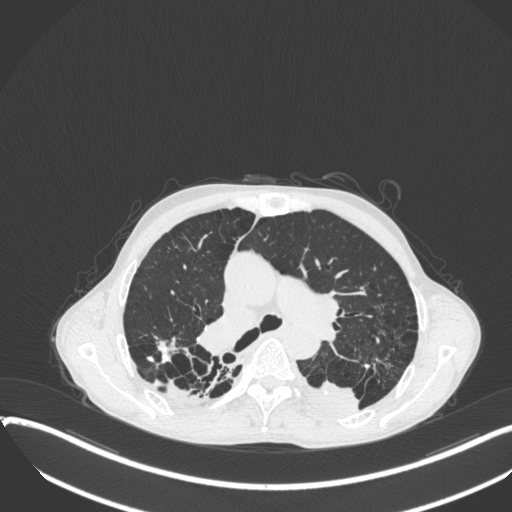
Chest CT, one axial slice. Slice 250 of 400 in the series (ordered by position). Reconstruction kernel B31f. Lung window (W 1500 / L -600 HU). 512 × 512 image matrix, field of view 400 × 400 mm. Male patient, age 57 years. From the clinical record (not read from this slice): clinical TNM (as recorded): T4 N0 M0.
Structures marked on this image (bounding box drawn by a radiologist):
- lung tumour (recorded histology: squamous cell carcinoma): bounding box [x1, y1, x2, y2] px = [301, 375, 361, 419]